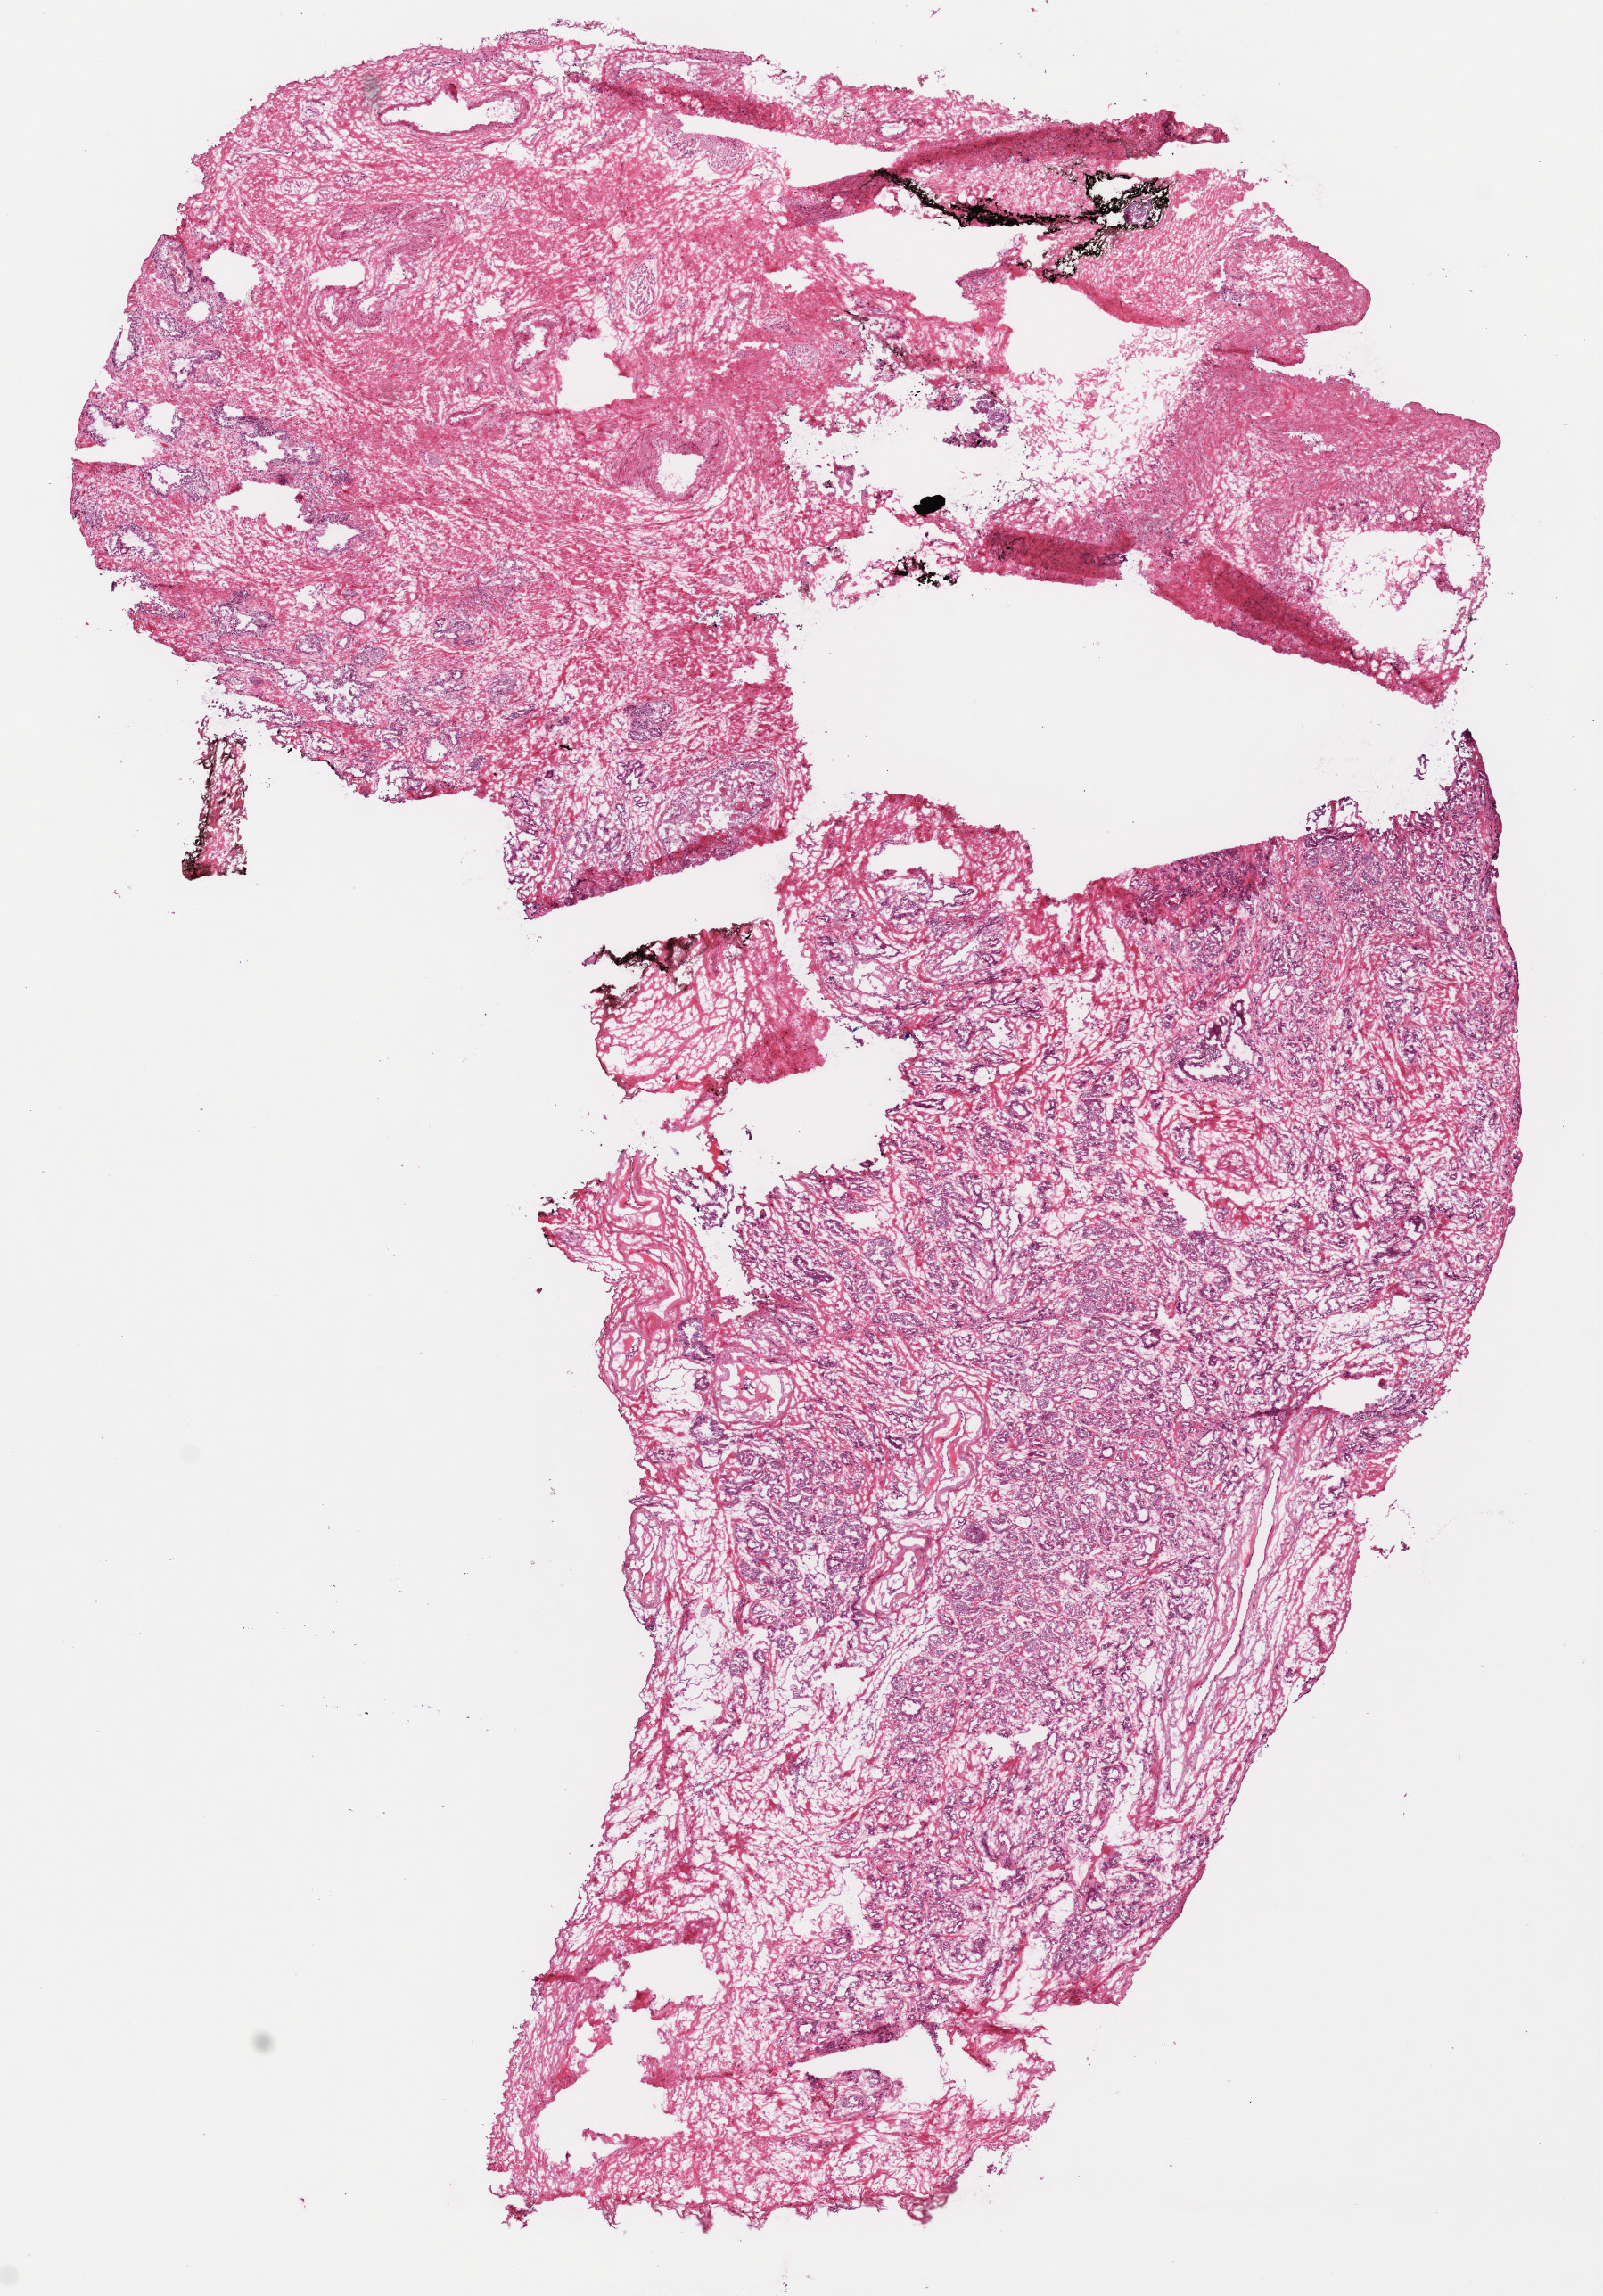
H&E whole-slide image — low-resolution overview of the scanned area, about 7.3 x 10.4 mm (acquisition: 40x scan); frozen section from the top of the tissue portion; prostate, primary tumour sample. Male, age 61 years at initial diagnosis. Gleason score: 7 (3+4). Pathologist review of this section (percent, as recorded): tumour cells 60%, tumour nuclei 70%, normal cells 0%, stromal cells 40%, necrosis 0%. Infiltration values recorded for this section: lymphocyte infiltration 0%, monocyte infiltration 0%, neutrophil infiltration 0%.
Histologic diagnosis: Adenocarcinoma, NOS (prostate gland).